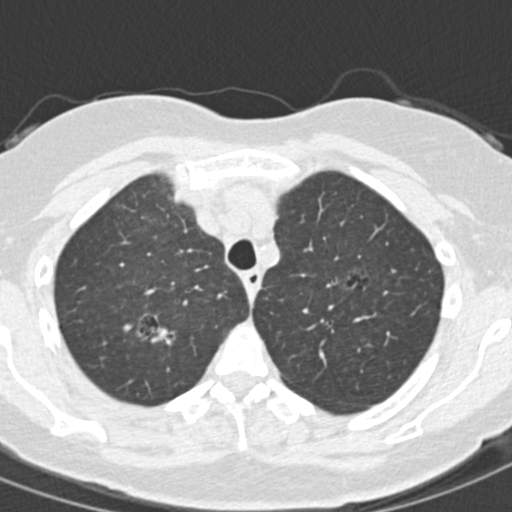
Low-dose screening chest CT, one axial slice; position 122 of 157 along the scan axis; reconstruction kernel B30f; lung window (W 1500 / L -600 HU); 512 × 512 image matrix, field of view 280 × 280 mm.
Structures marked on this image (manually delineated by an expert):
- lesion 1 (tumor, upper lobe of right lung): box from (x=123, y=313) to (x=177, y=347) px